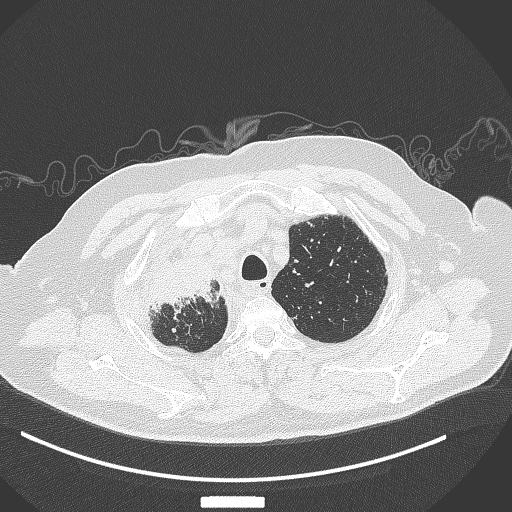
Chest CT, one axial slice; slice 312 of 384 in the series (ordered by position); 120 kVp; lung window (W 1500 / L -600 HU); 1 mm slice thickness; 512 × 512 image matrix, field of view 400 × 400 mm. Patient: male, 69 years. From the clinical record (not read from this slice): clinical TNM (as recorded): T4 N3 M1.
Outlined on this slice (bounding box drawn by a radiologist):
- lung tumour (recorded histology: adenocarcinoma): box from (x=147, y=253) to (x=222, y=318) px